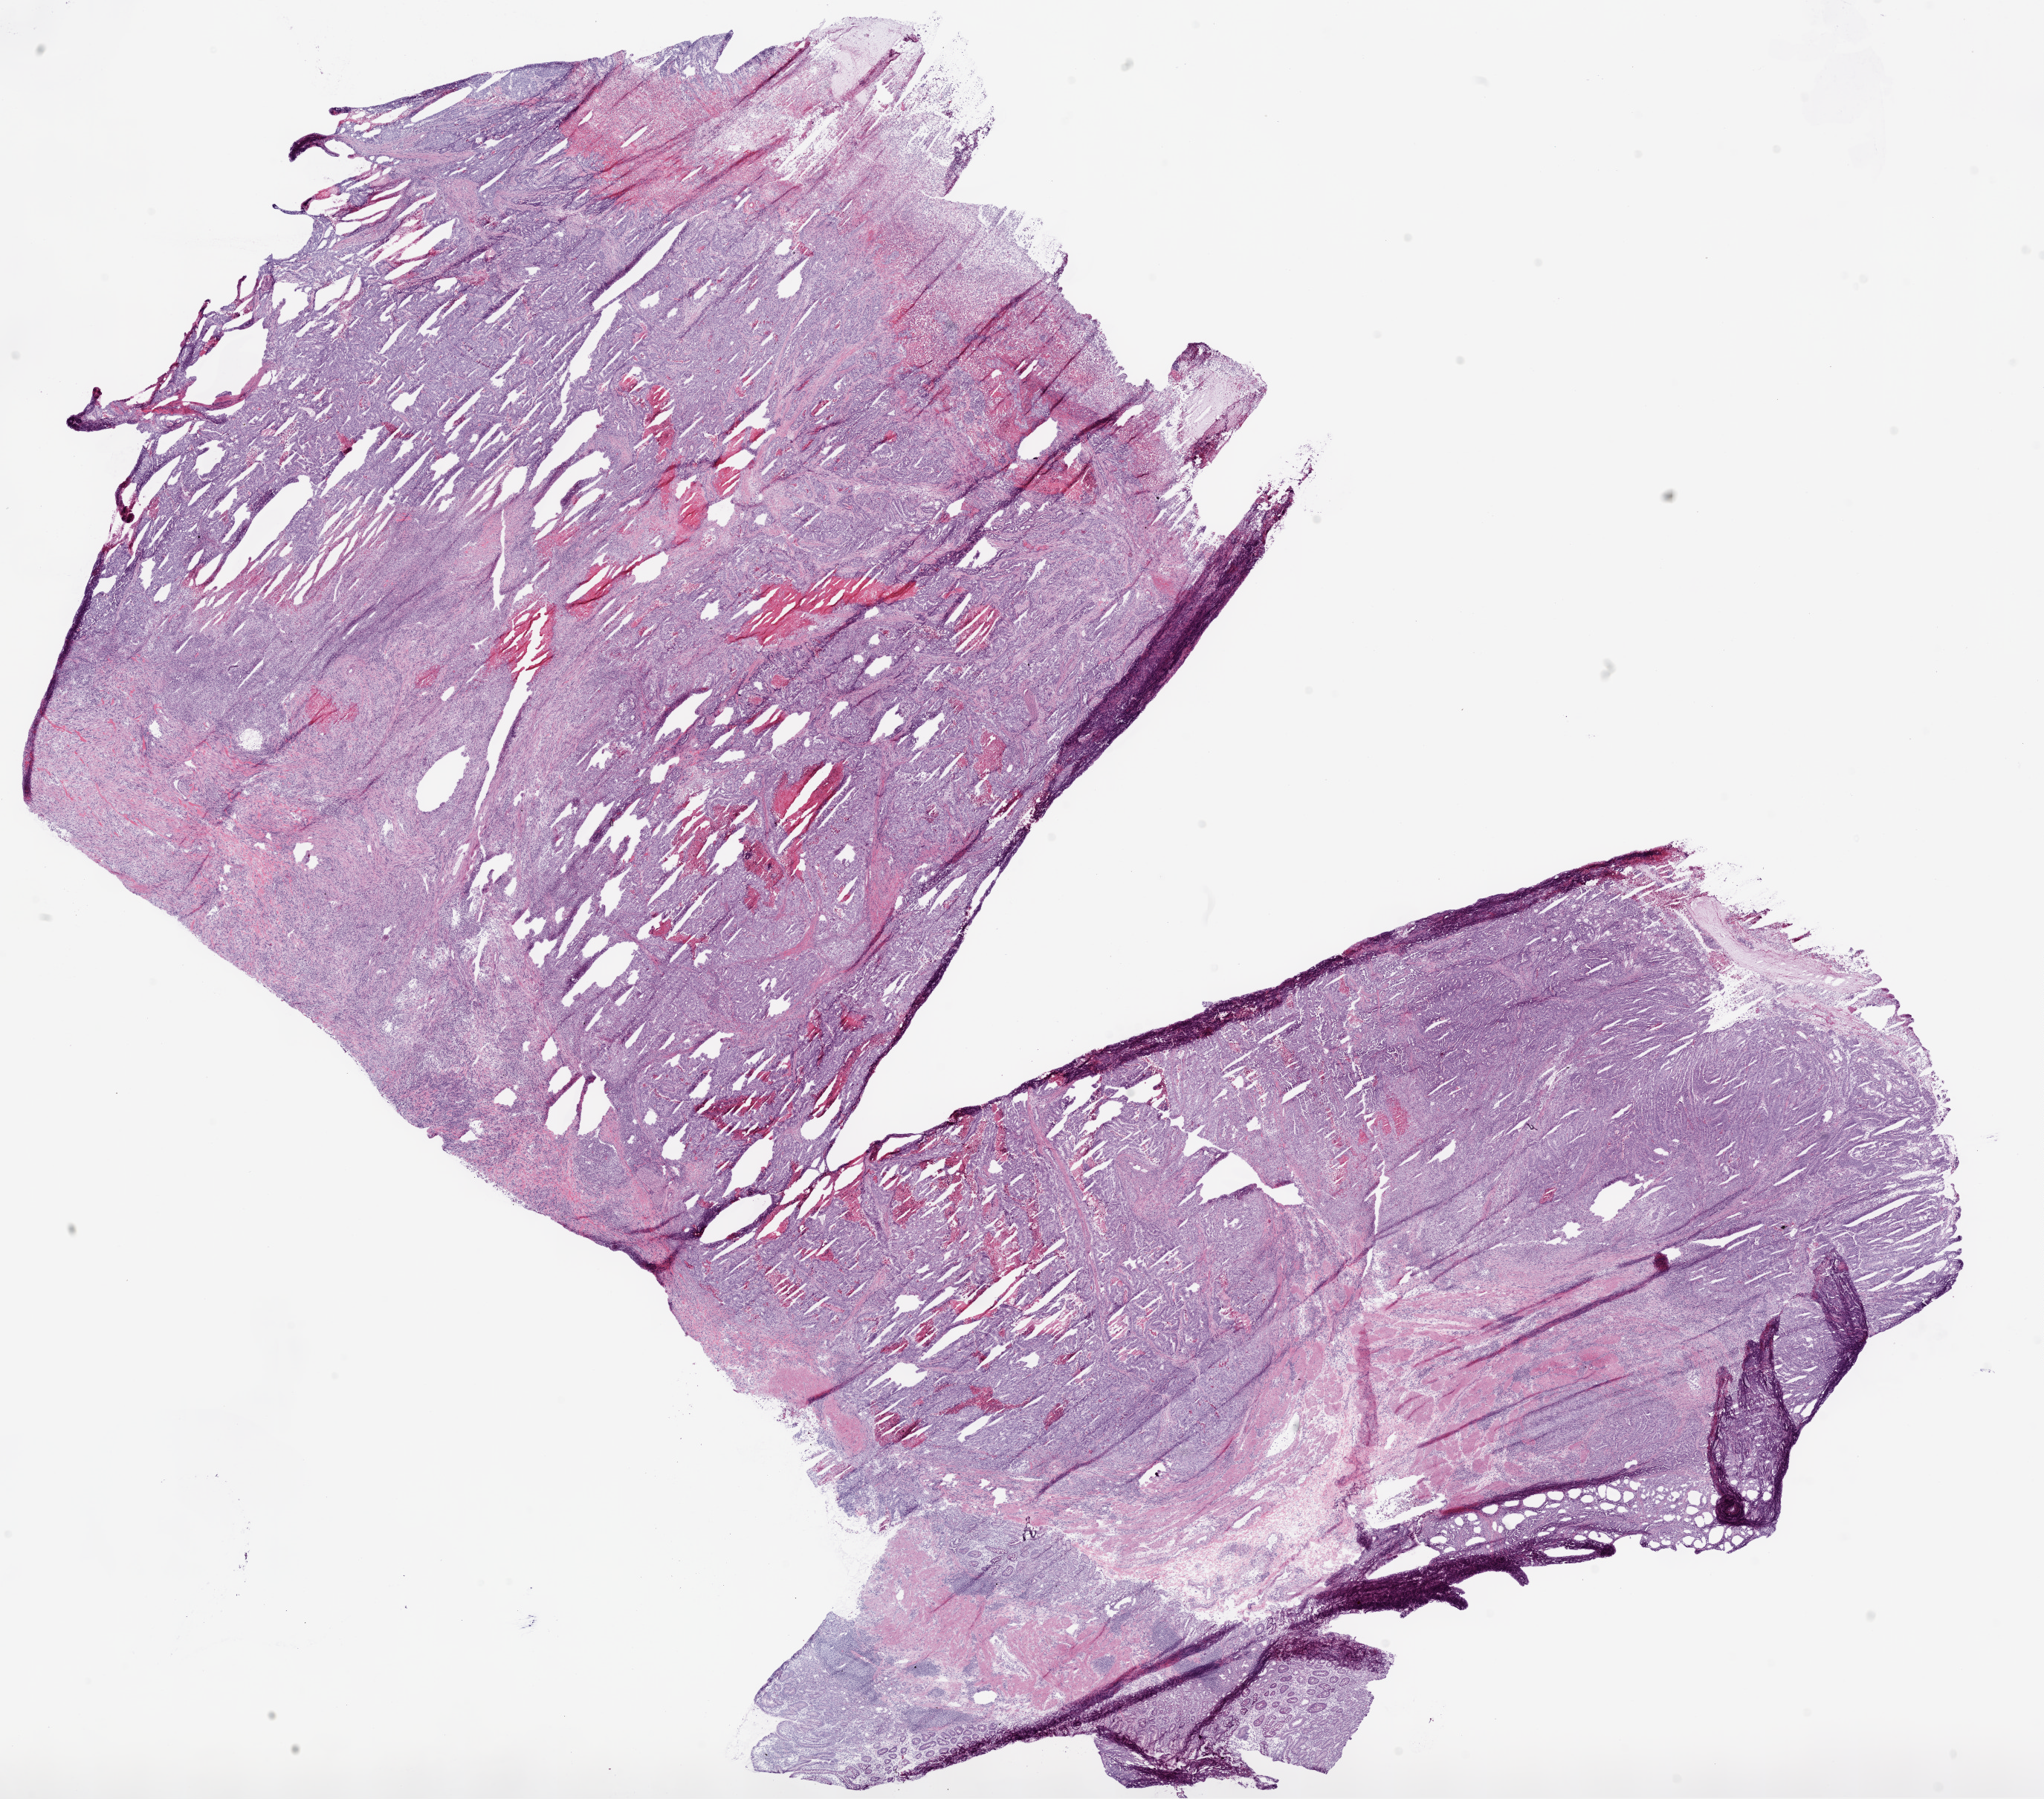
Hematoxylin and eosin (H&E) stained whole-slide image — whole scanned area (about 22.1 x 19.4 mm, acquisition: 20x scan) shown as a low-resolution overview, frozen section from the top of the tissue portion, stomach, primary tumour sample. Male patient; age at initial diagnosis 58 years. Histologic grade: G2 (moderately differentiated). Slide review estimates, as recorded: tumour cells 80%, tumour nuclei 70%, normal cells 0%, stromal cells 10%, necrosis 10%.
• histologic diagnosis: Adenocarcinoma, NOS (body of stomach)